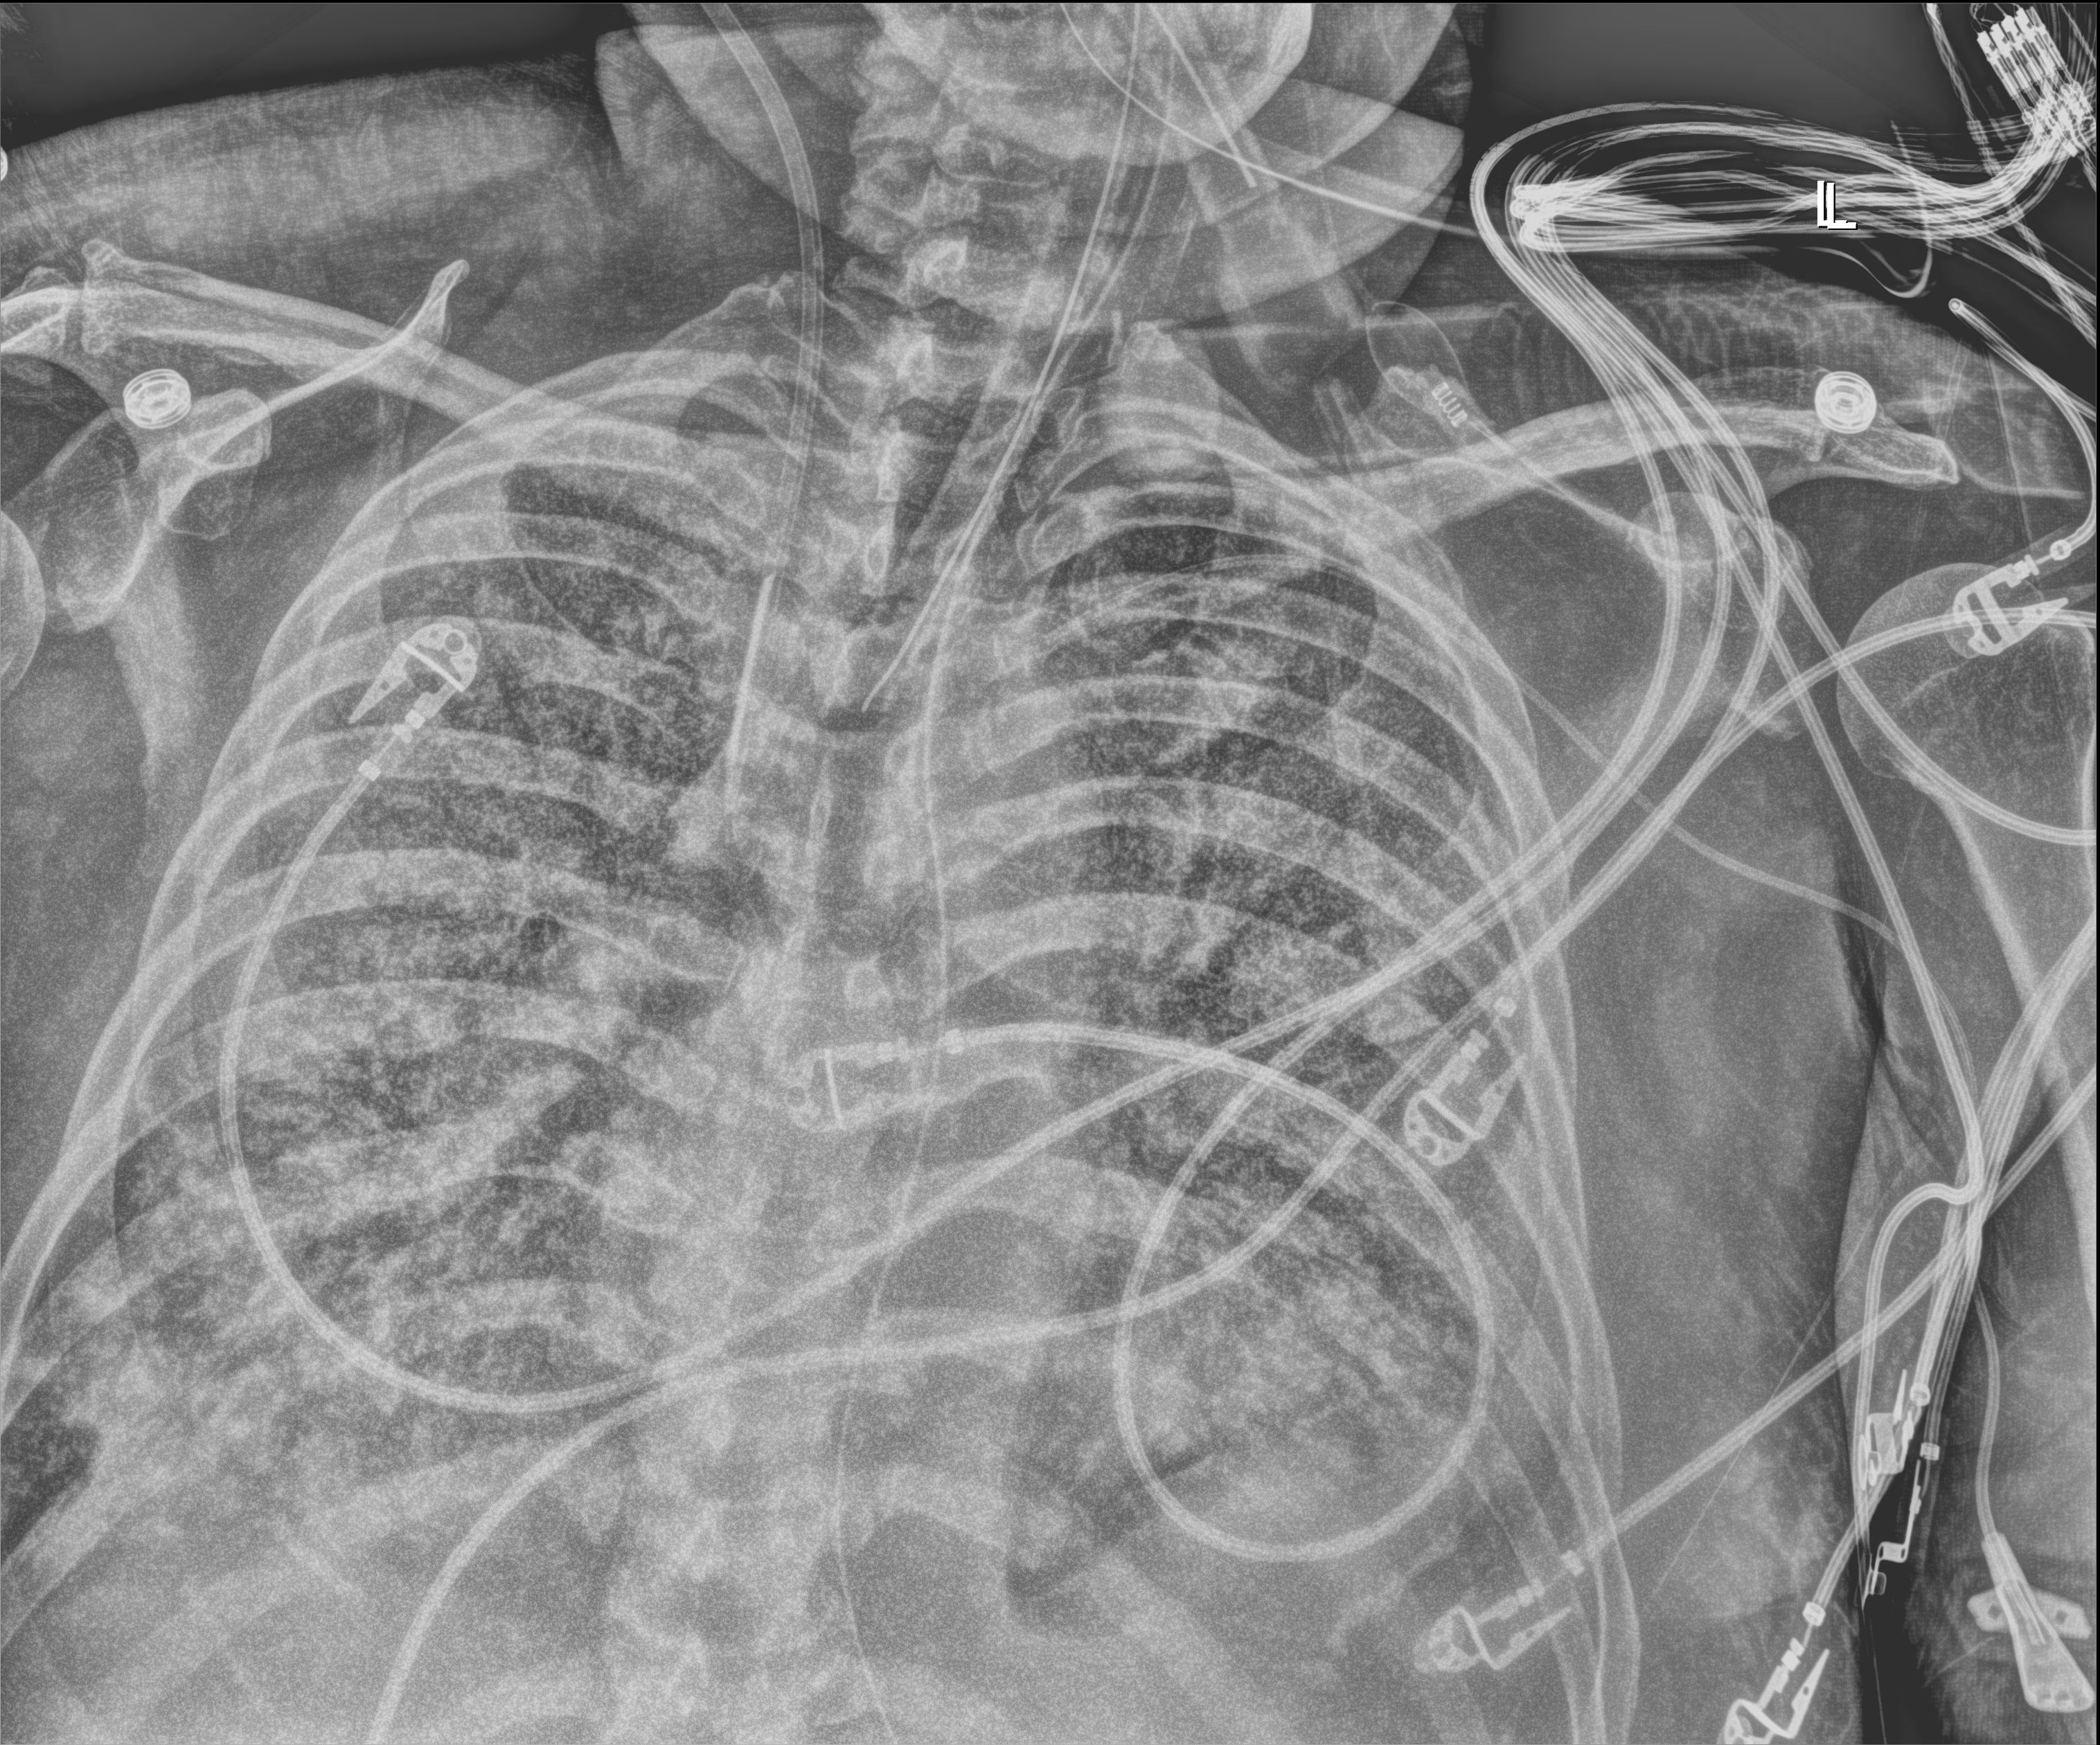
Bedside chest radiograph (digital radiography), anteroposterior (AP) projection. Patient hospitalised with COVID-19; male, aged 60–74 years.
From the hospital-stay record, not from the radiograph (when in the stay this image was taken is not recorded): mechanically ventilated during this hospital stay: yes.